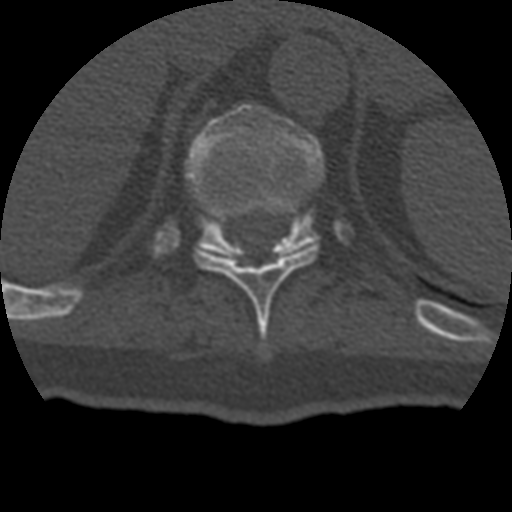
CT including the spine, one axial slice. Slice 209 of 399 in the series (ordered by position). Bone window (W 1800 / L 400 HU). 512 × 512 image matrix, field of view 160 × 160 mm. Patient age 69 years. From the clinical record (not read from this slice): primary cancer: prostate.
Outlined on this slice (semi-automatic segmentation, software-assisted and operator-edited):
- T10 vertebra: box from (x=195, y=247) to (x=318, y=346) px
- T11 vertebra: (x=186, y=104)–(x=324, y=260)